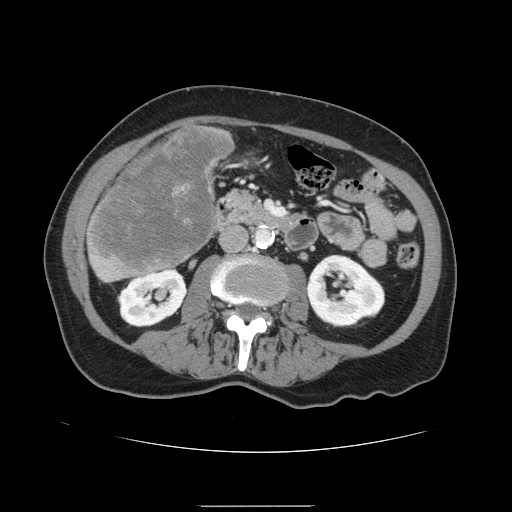
Contrast-enhanced abdominal CT, one axial slice. Slice 42 of 168 in the series (ordered by position). 120 kVp. Soft-tissue window (W 400 / L 40 HU). 512 × 512 image matrix, field of view 386 × 386 mm. Male patient, age 74 years. From the clinical record (not read from this slice): diagnosis: colorectal cancer liver metastases, imaged before liver resection; multiple liver metastases: no; largest metastasis: 14.5 cm; disease in both lobes: yes.
Annotated regions visible in this slice (outlined manually by an expert reader):
- liver: box from (x=86, y=125) to (x=233, y=283) px
- liver metastasis: (x=90, y=128)–(x=231, y=271)